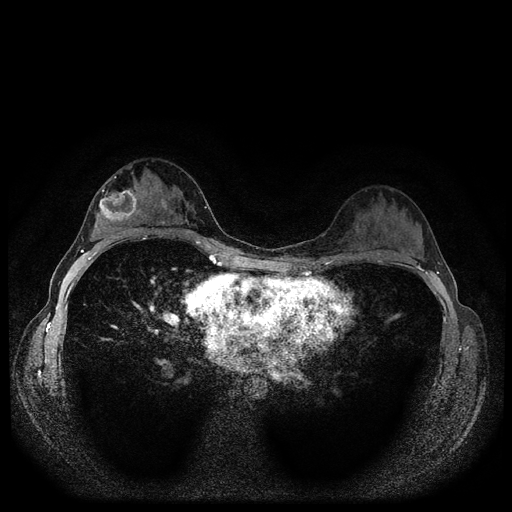
Breast MRI (dynamic contrast-enhanced, multi-phase), one axial slice. Slice 64 of 116 in the series (ordered by position). Dynamic contrast-enhanced series, time point 2 of 5 at this slice position (early post-contrast). 1.5 T. TE 2.7 ms, TR 5.4 ms. 512 × 512 image matrix, field of view 320 × 320 mm. Female patient, age 29 years.
Annotated regions visible in this slice (semi-automatic segmentation, software-assisted and operator-edited):
- breast lesion (labelled benign in the annotation): bounding box [x1, y1, x2, y2] px = [158, 196, 170, 214]
- breast lesion (labelled 'tumour' in the annotation; benign lesions carry a separate 'benign' label): [96, 187, 139, 224]